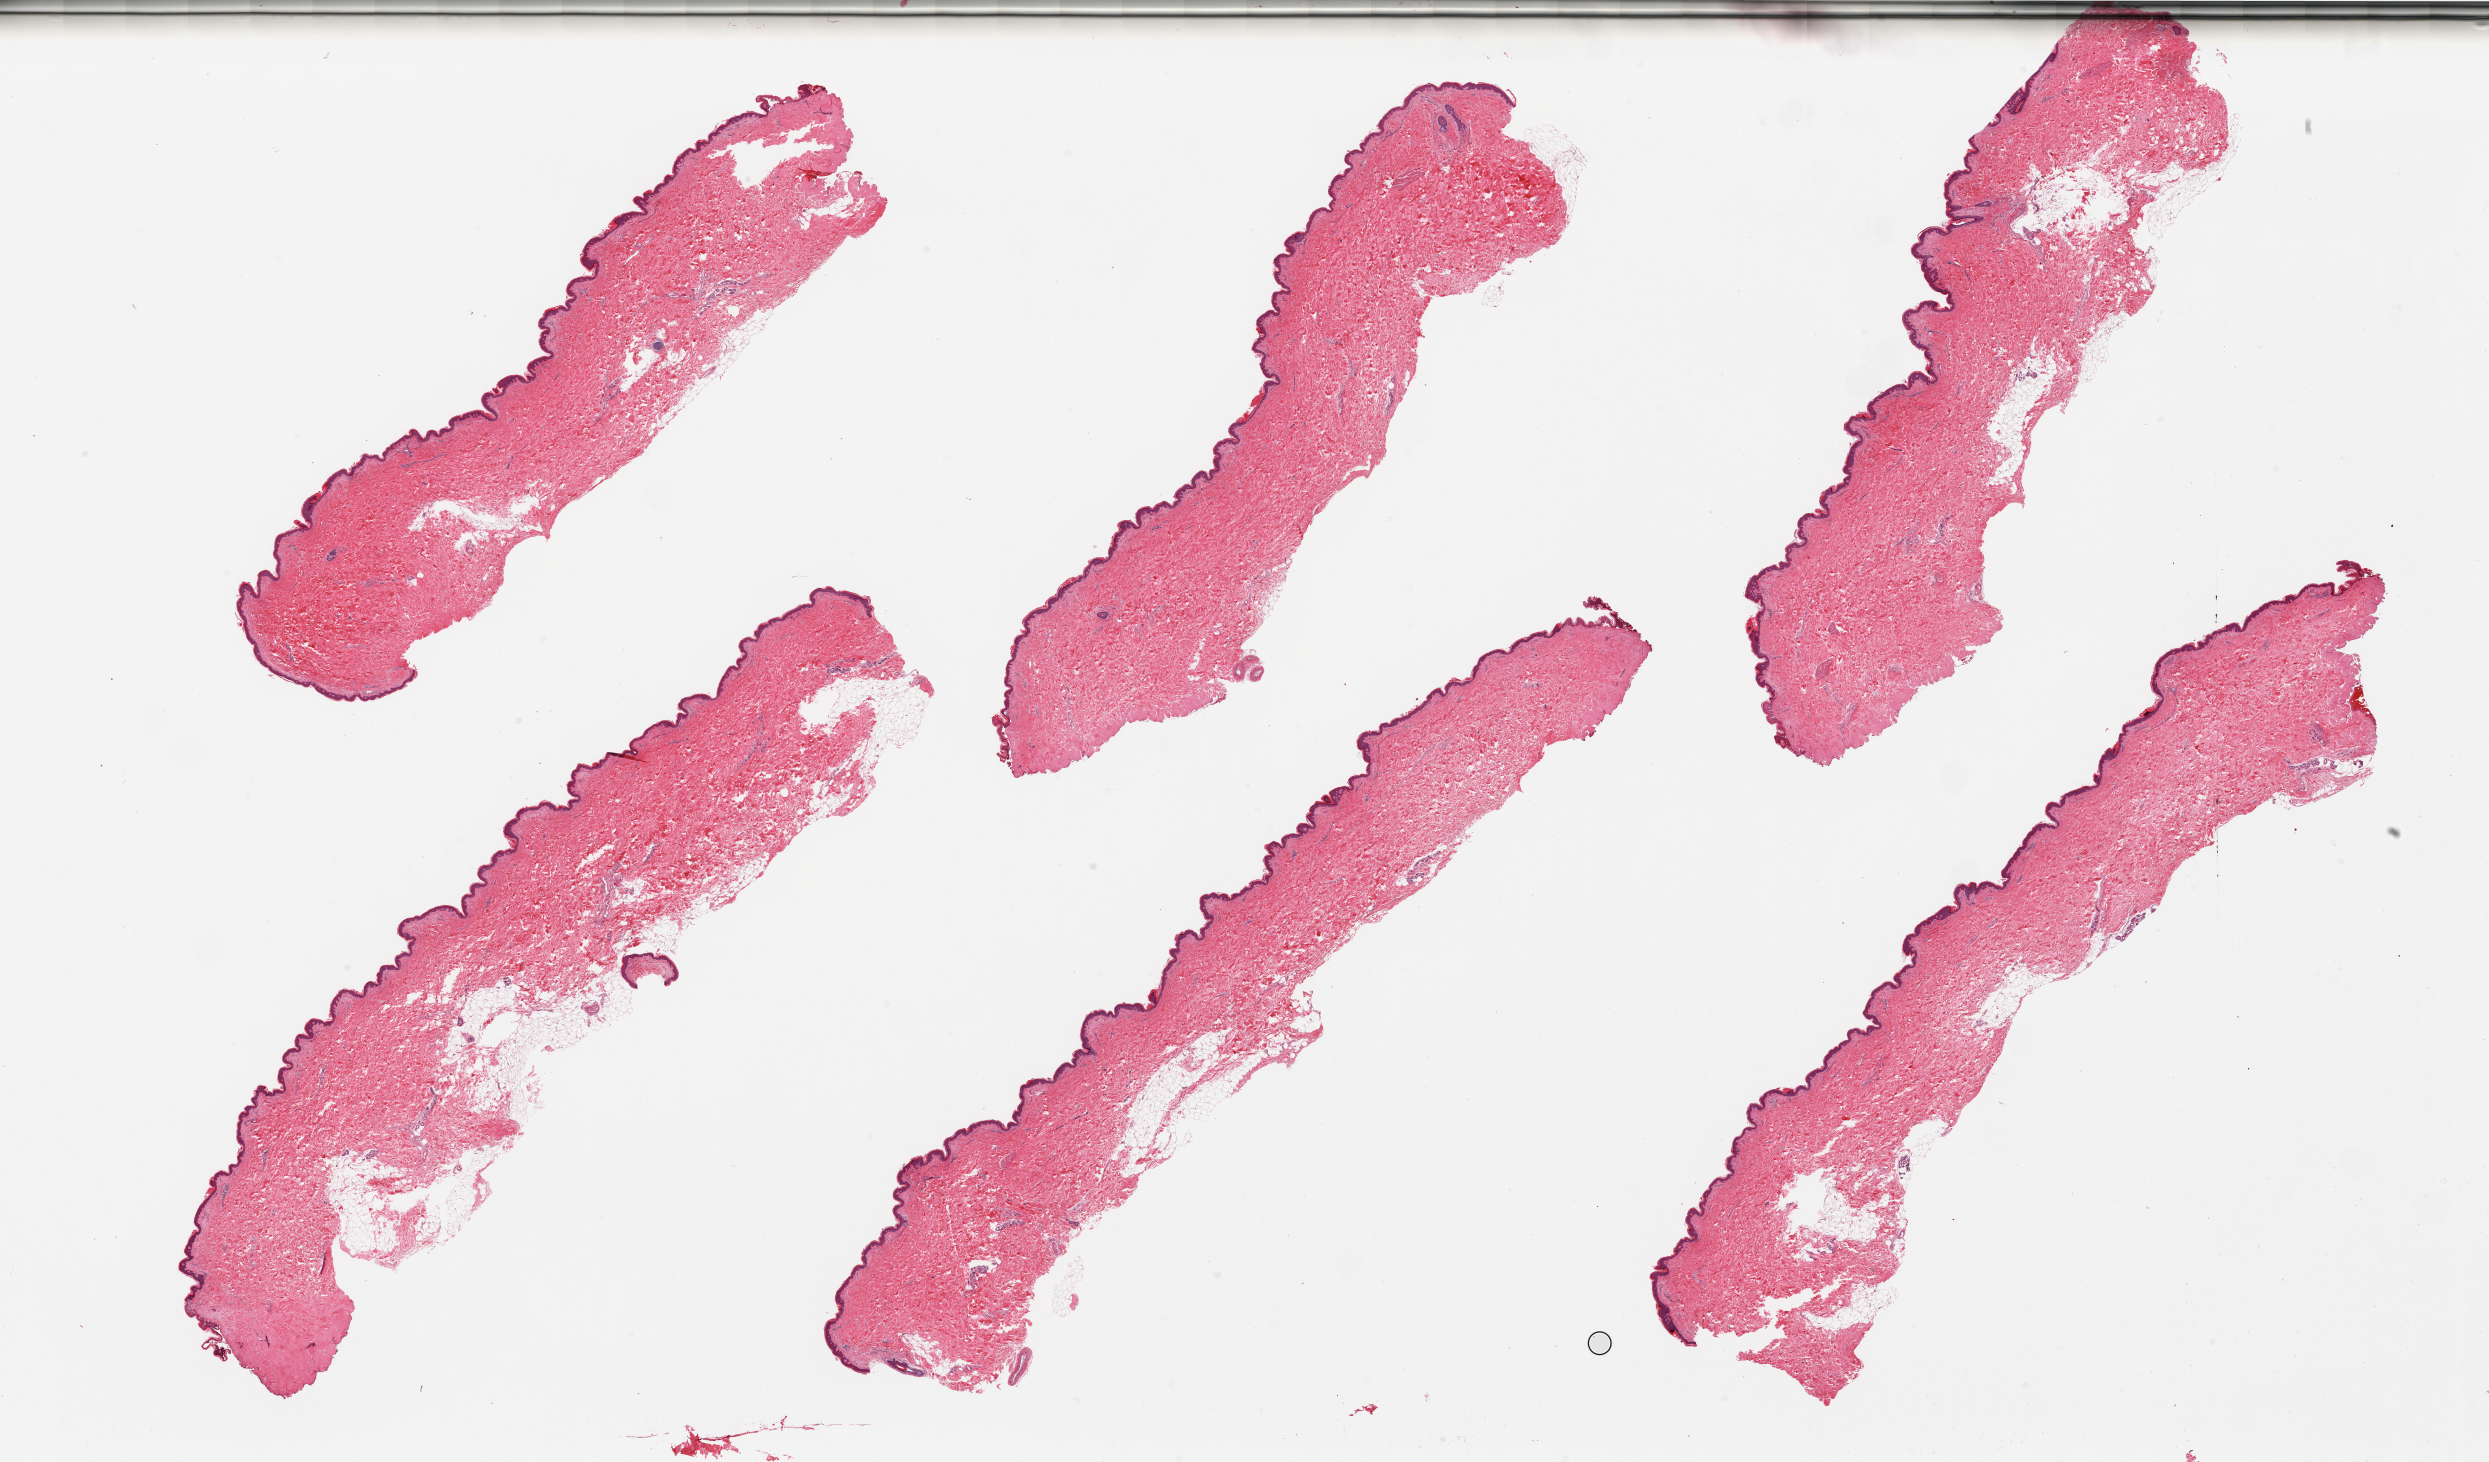
Digitized H&E-stained section, shown as a low-resolution overview of the whole scanned area (about 39.4 x 23.1 mm, from a 20x scan), PAXgene-fixed, paraffin-embedded tissue, sampled site (target tissue): skin of suprapubic region, donor tissue sample. Donor: female.
Reviewer comment on this tissue sample: 6 pieces. Well trimmed.